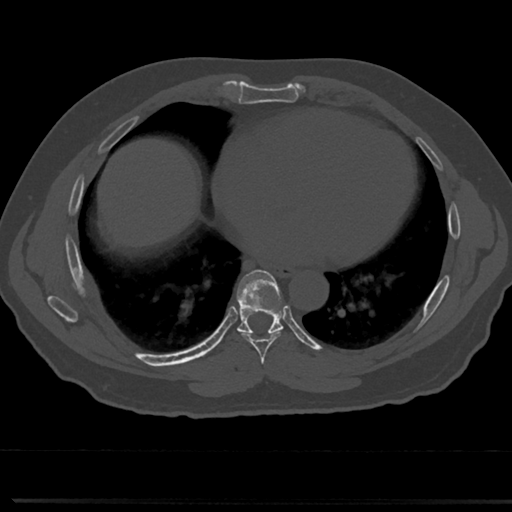
CT including the spine, one axial slice; slice 380 of 817 in the series (ordered by position); 120 kVp; bone window (W 1800 / L 400 HU); 0.5 mm slice thickness; 512 × 512 image matrix. Patient: male, 61 years. Case-level facts recorded for this patient, not image findings: primary cancer: prostate.
Outlined on this slice (semi-automatic segmentation, software-assisted and operator-edited):
- T6 vertebra: bounding box (x1, y1, x2, y2) in pixels: (260, 368, 267, 376)
- T7 vertebra: (230, 273, 304, 353)